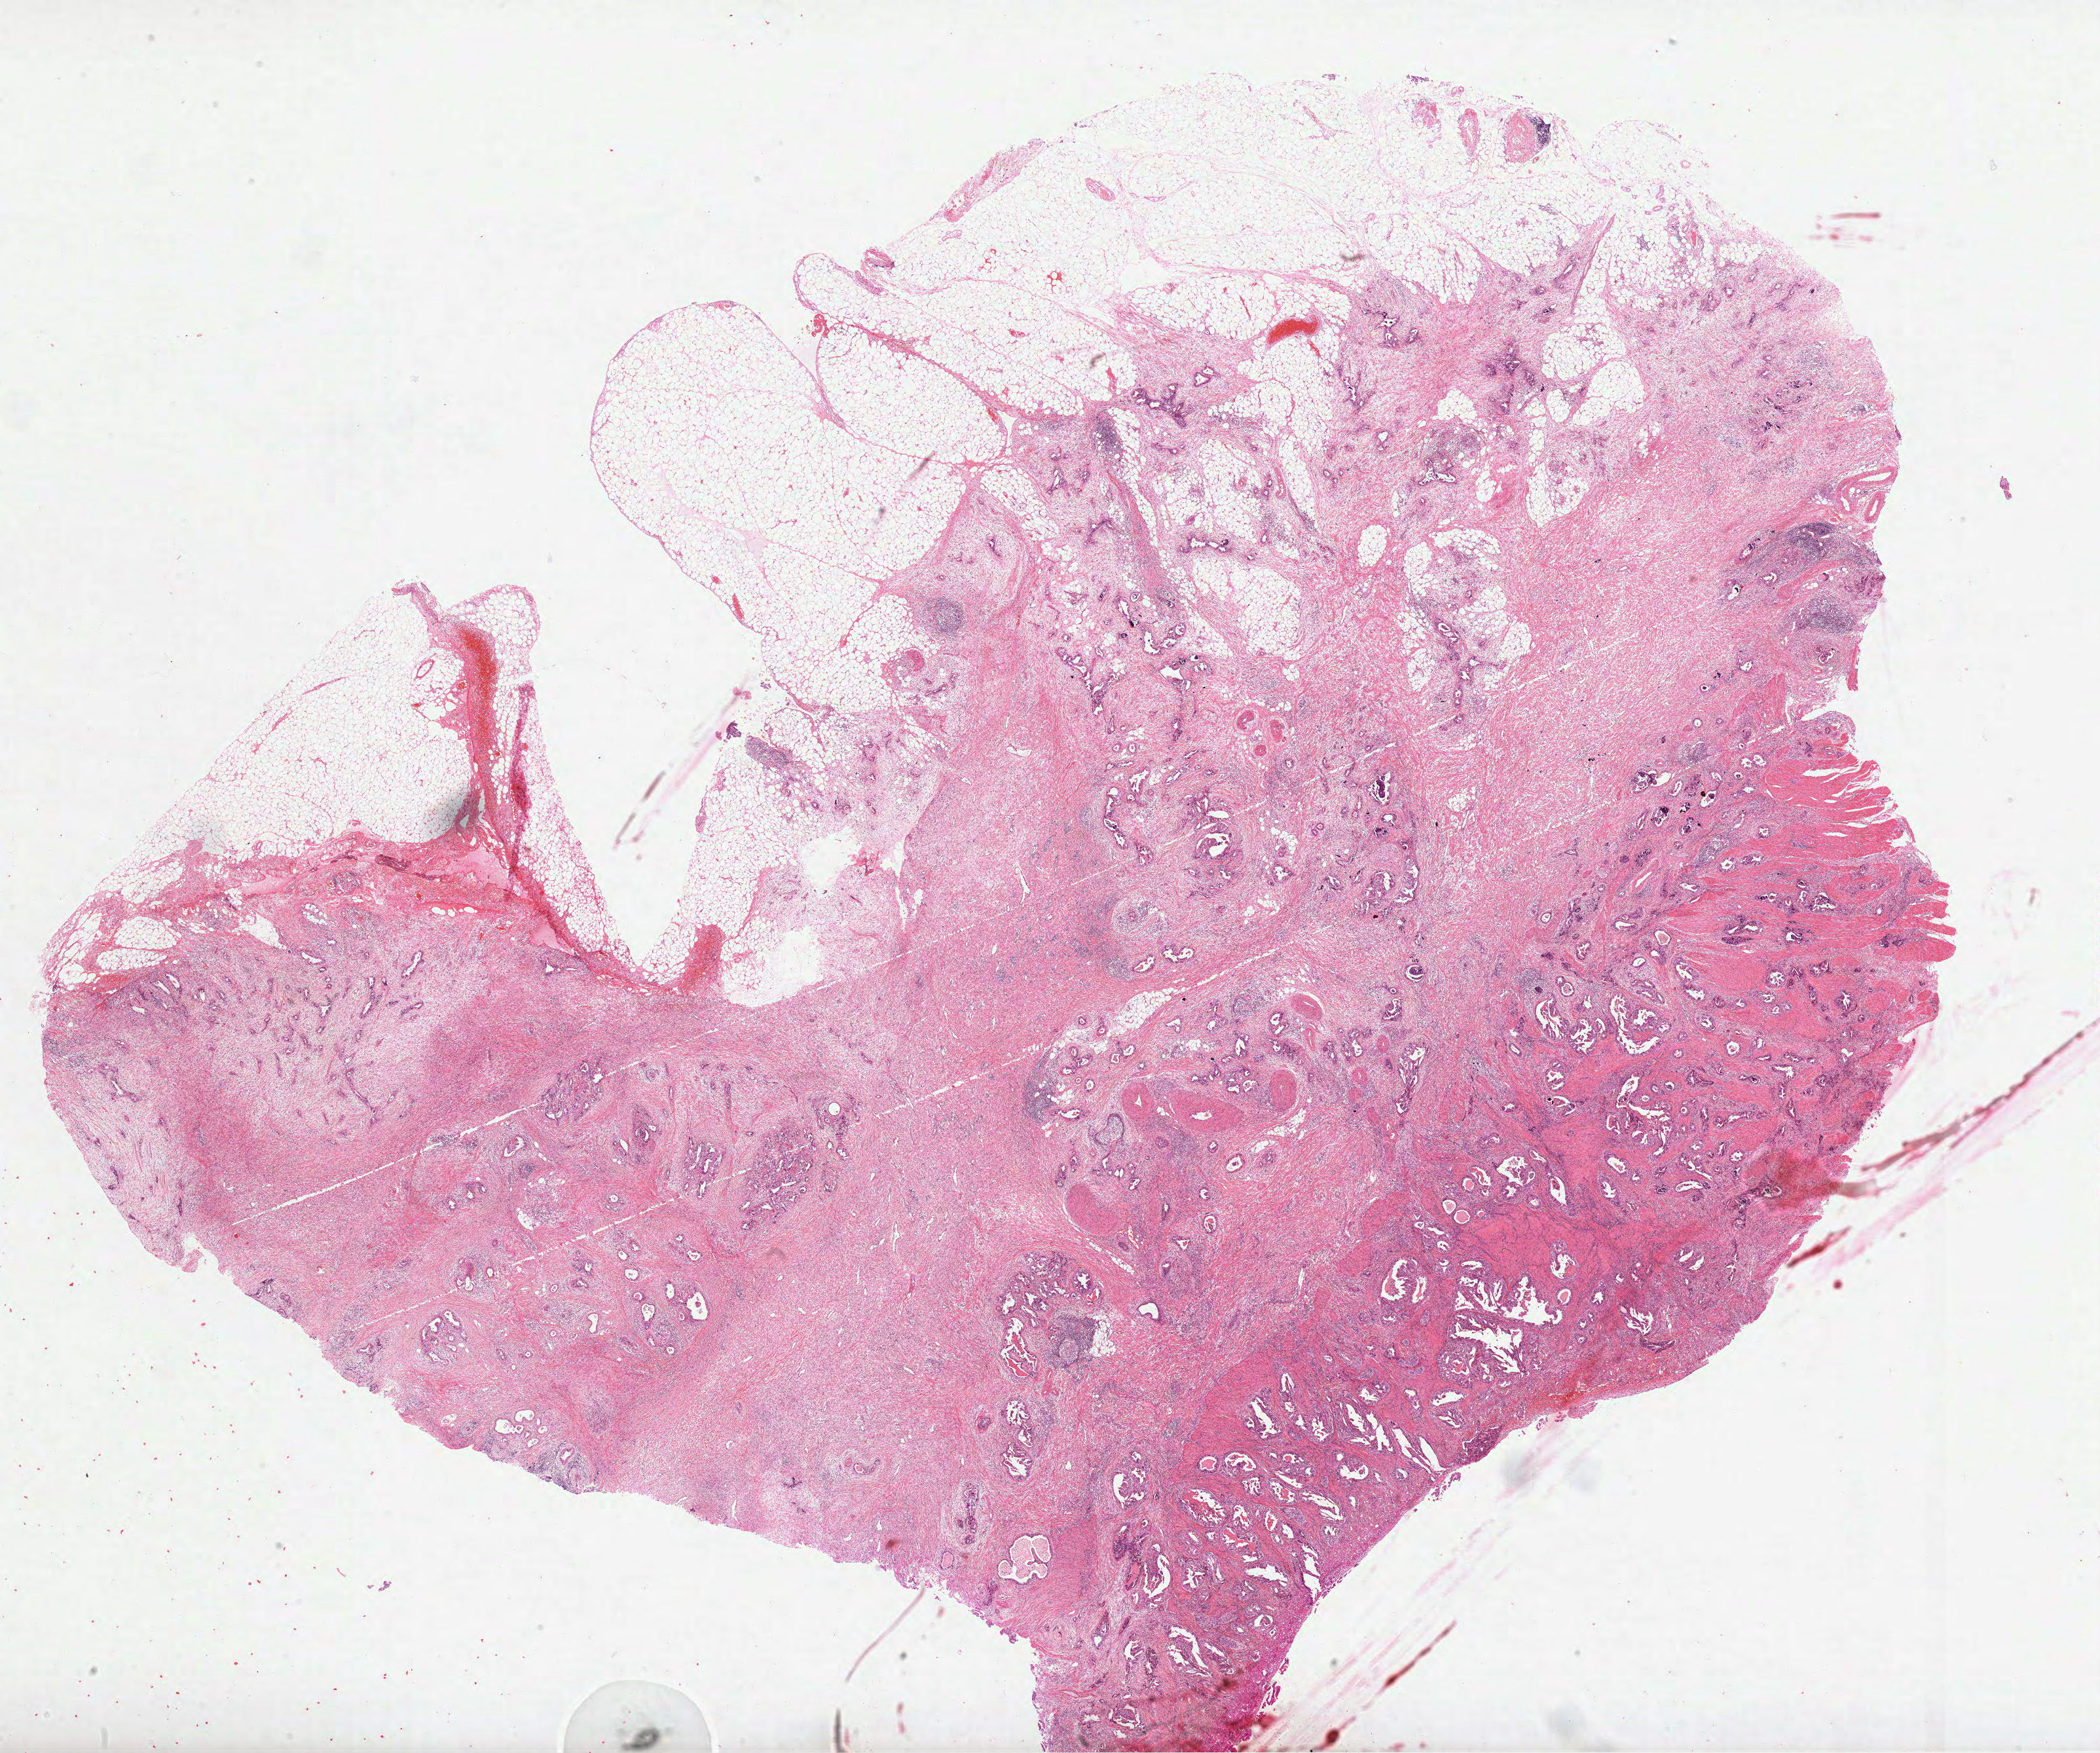
Hematoxylin and eosin (H&E) stained whole-slide image, a low-resolution overview of the entire scanned area, about 25.9 x 21.6 mm (slide scanned at 40x), formalin-fixed paraffin-embedded (FFPE) diagnostic section, stomach, primary tumour sample. Patient: male, age at initial diagnosis 59 years. Histologic grade: G2 (moderately differentiated).
• histologic diagnosis: Adenocarcinoma, intestinal type (gastric antrum)
• AJCC pathologic stage: IIIA